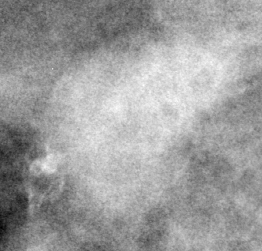
Cropped region of a digitized screen-film mammogram centred on a radiologist-marked abnormality, right breast, CC view.
Finding: mass, shape irregular, margins obscured / ill defined; BI-RADS assessment category 4; subtlety rating 3 on a 1 (subtle) to 5 (obvious) scale; pathology (as recorded): malignant.